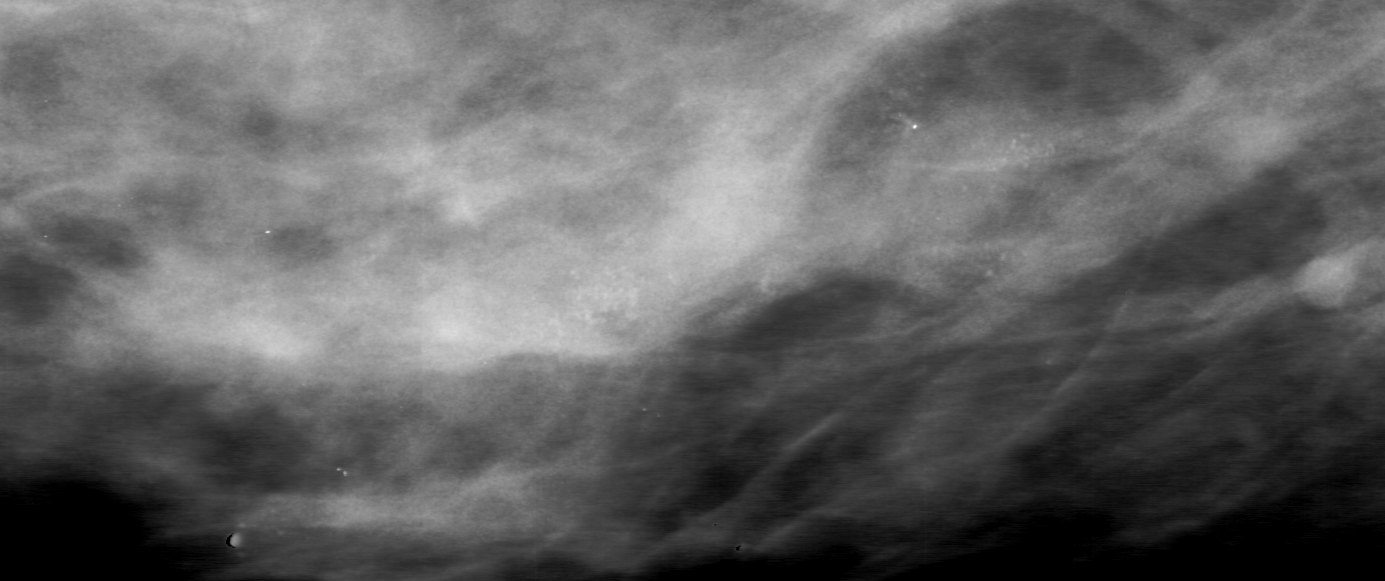
Region of interest cut from a scanned film mammogram (one marked finding), right breast, MLO view, BI-RADS breast density category 3 (scale 1–4).
Marked abnormality: calcifications, morphology amorphous, distribution segmental; BI-RADS assessment category 5; pathology (as recorded): malignant.